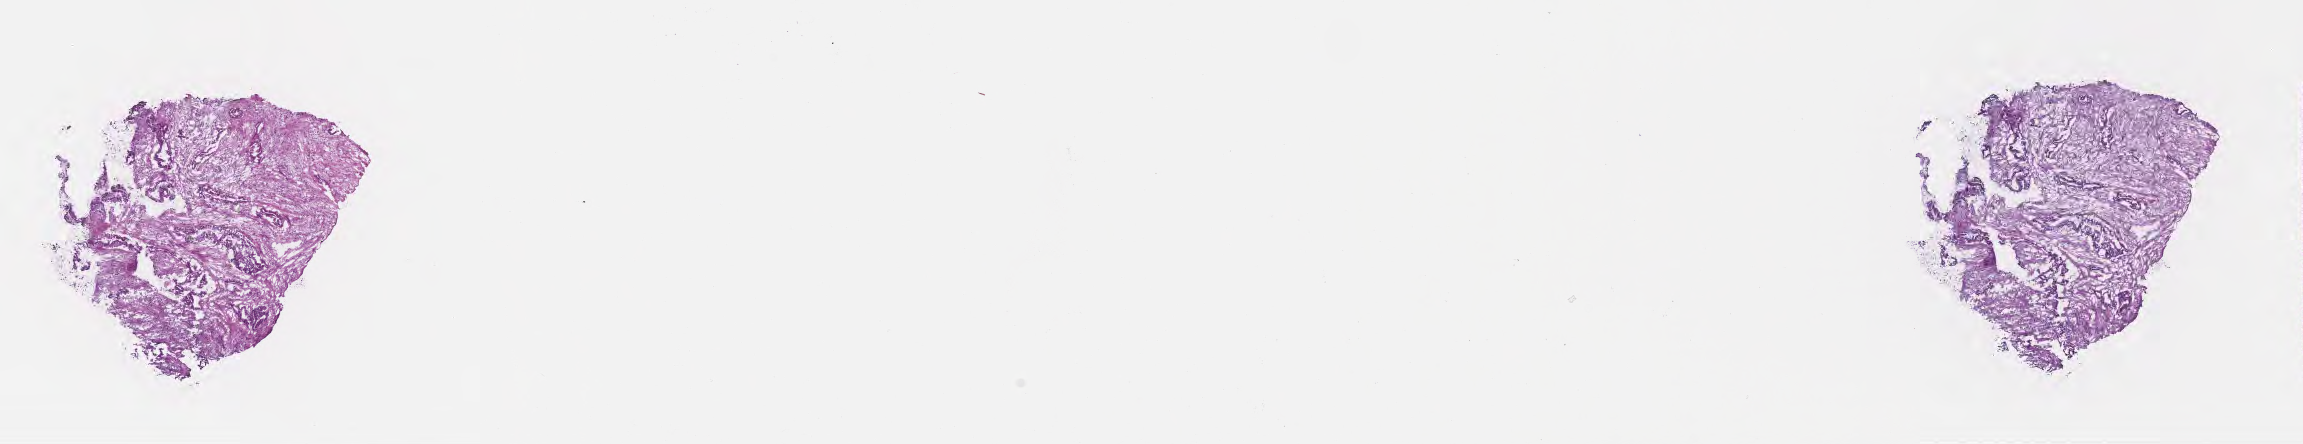
Whole-slide image, haematoxylin and eosin stain, low-resolution overview of the scanned area, about 18.6 x 3.6 mm, frozen section (tissue freezing medium), primary tumor, site: body of pancreas. Patient: male, age at initial diagnosis 72 years. Composition of this section per pathologist review: tumor cells 100%, tumor nuclei 35%, stromal cells 0%, necrosis 0%, normal cells 0%. Infiltration values recorded for this section: lymphocyte infiltration 0%, monocyte infiltration 0%, neutrophil infiltration 0%.
Diagnosis: Adenocarcinoma, NOS. AJCC pathologic stage: Stage IIB. Section: bottom of the tissue portion.